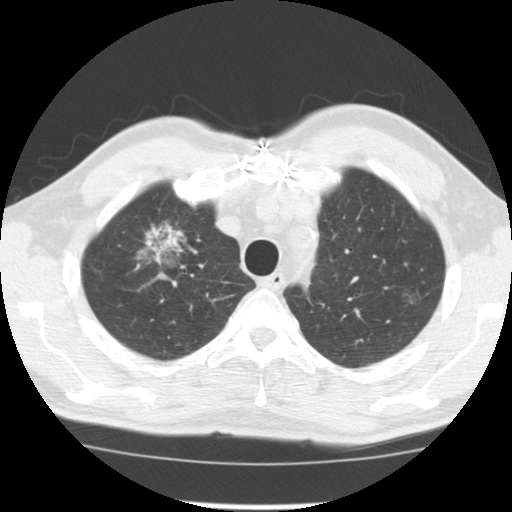
Axial slice from a low-dose chest CT screening exam, third annual screen, lung window (W 1500 / L -600 HU), standard (soft-tissue) reconstruction kernel (STANDARD), 512 × 512 image matrix, field of view 340 × 340 mm. Male, age 64 years at enrolment.
Expert reader's lesion annotation, box from (x=126, y=222) to (x=202, y=285) px. The screening reader recorded 3 non-calcified nodules or masses ≥4 mm on this exam (right upper lobe, right lower lobe, left upper lobe); which of them this box marks is not recorded. Official screen result: positive, other.